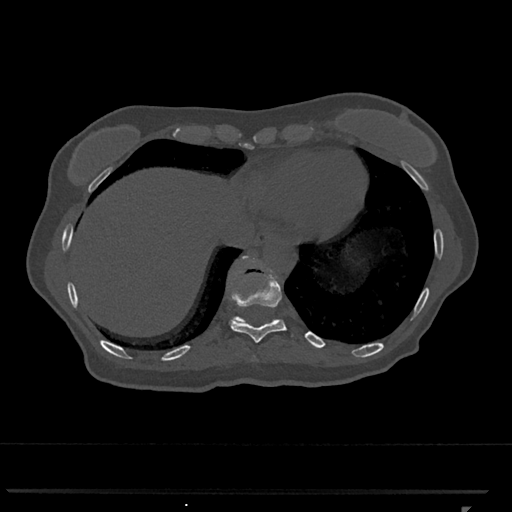
CT including the spine, one axial slice; position 562 of 793 along the scan axis; reconstruction kernel Br40s/3; bone window (W 1800 / L 400 HU); 0.5 mm slice thickness; 512 × 512 image matrix, field of view 380 × 380 mm. Patient: female, 62 years. Case-level facts recorded for this patient, not image findings: primary cancer: renal.
Outlined on this slice (semi-automatically segmented with operator editing):
- T10 vertebra: bounding box <229,263,287,343> (left, top, right, bottom; pixels)
- T11 vertebra: <232,255,275,323>